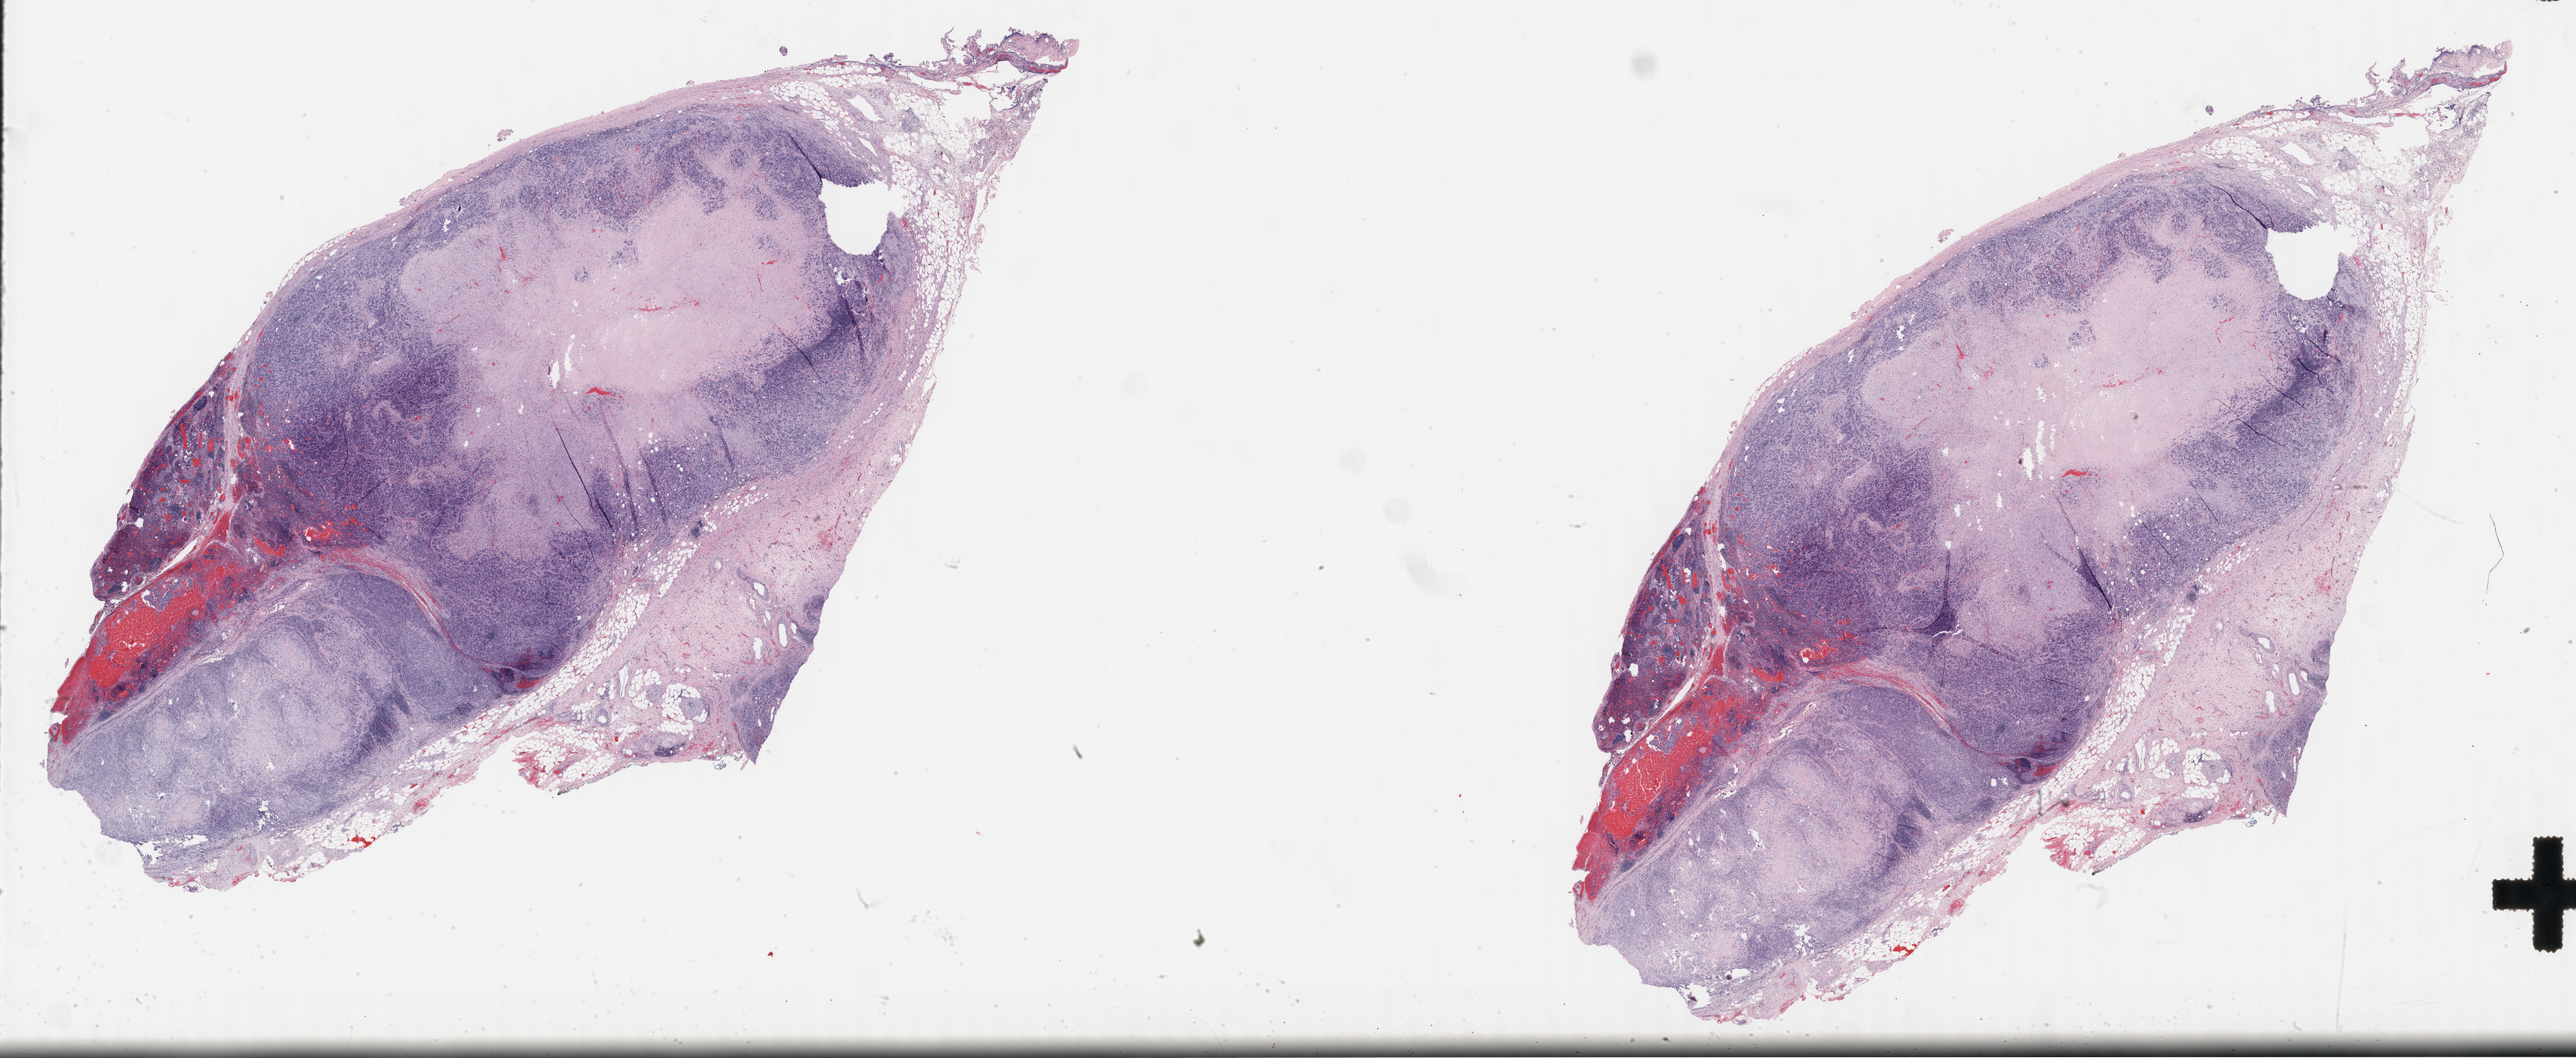
Whole-slide histology image, H&E-stained — shown as a low-resolution overview of the whole scanned area (about 47.3 x 19.4 mm, acquisition: 40x scan). FFPE section. Sample: primary tumour, pancreas. Female, age 48 years at initial diagnosis. Histologic grade: G3 (poorly differentiated).
* AJCC pathologic stage: IIB
* lymph nodes positive (case pathology): 2 of 11 examined
* TNM: T3 N1 M0
* diagnosis: Infiltrating duct carcinoma, NOS (head of pancreas)